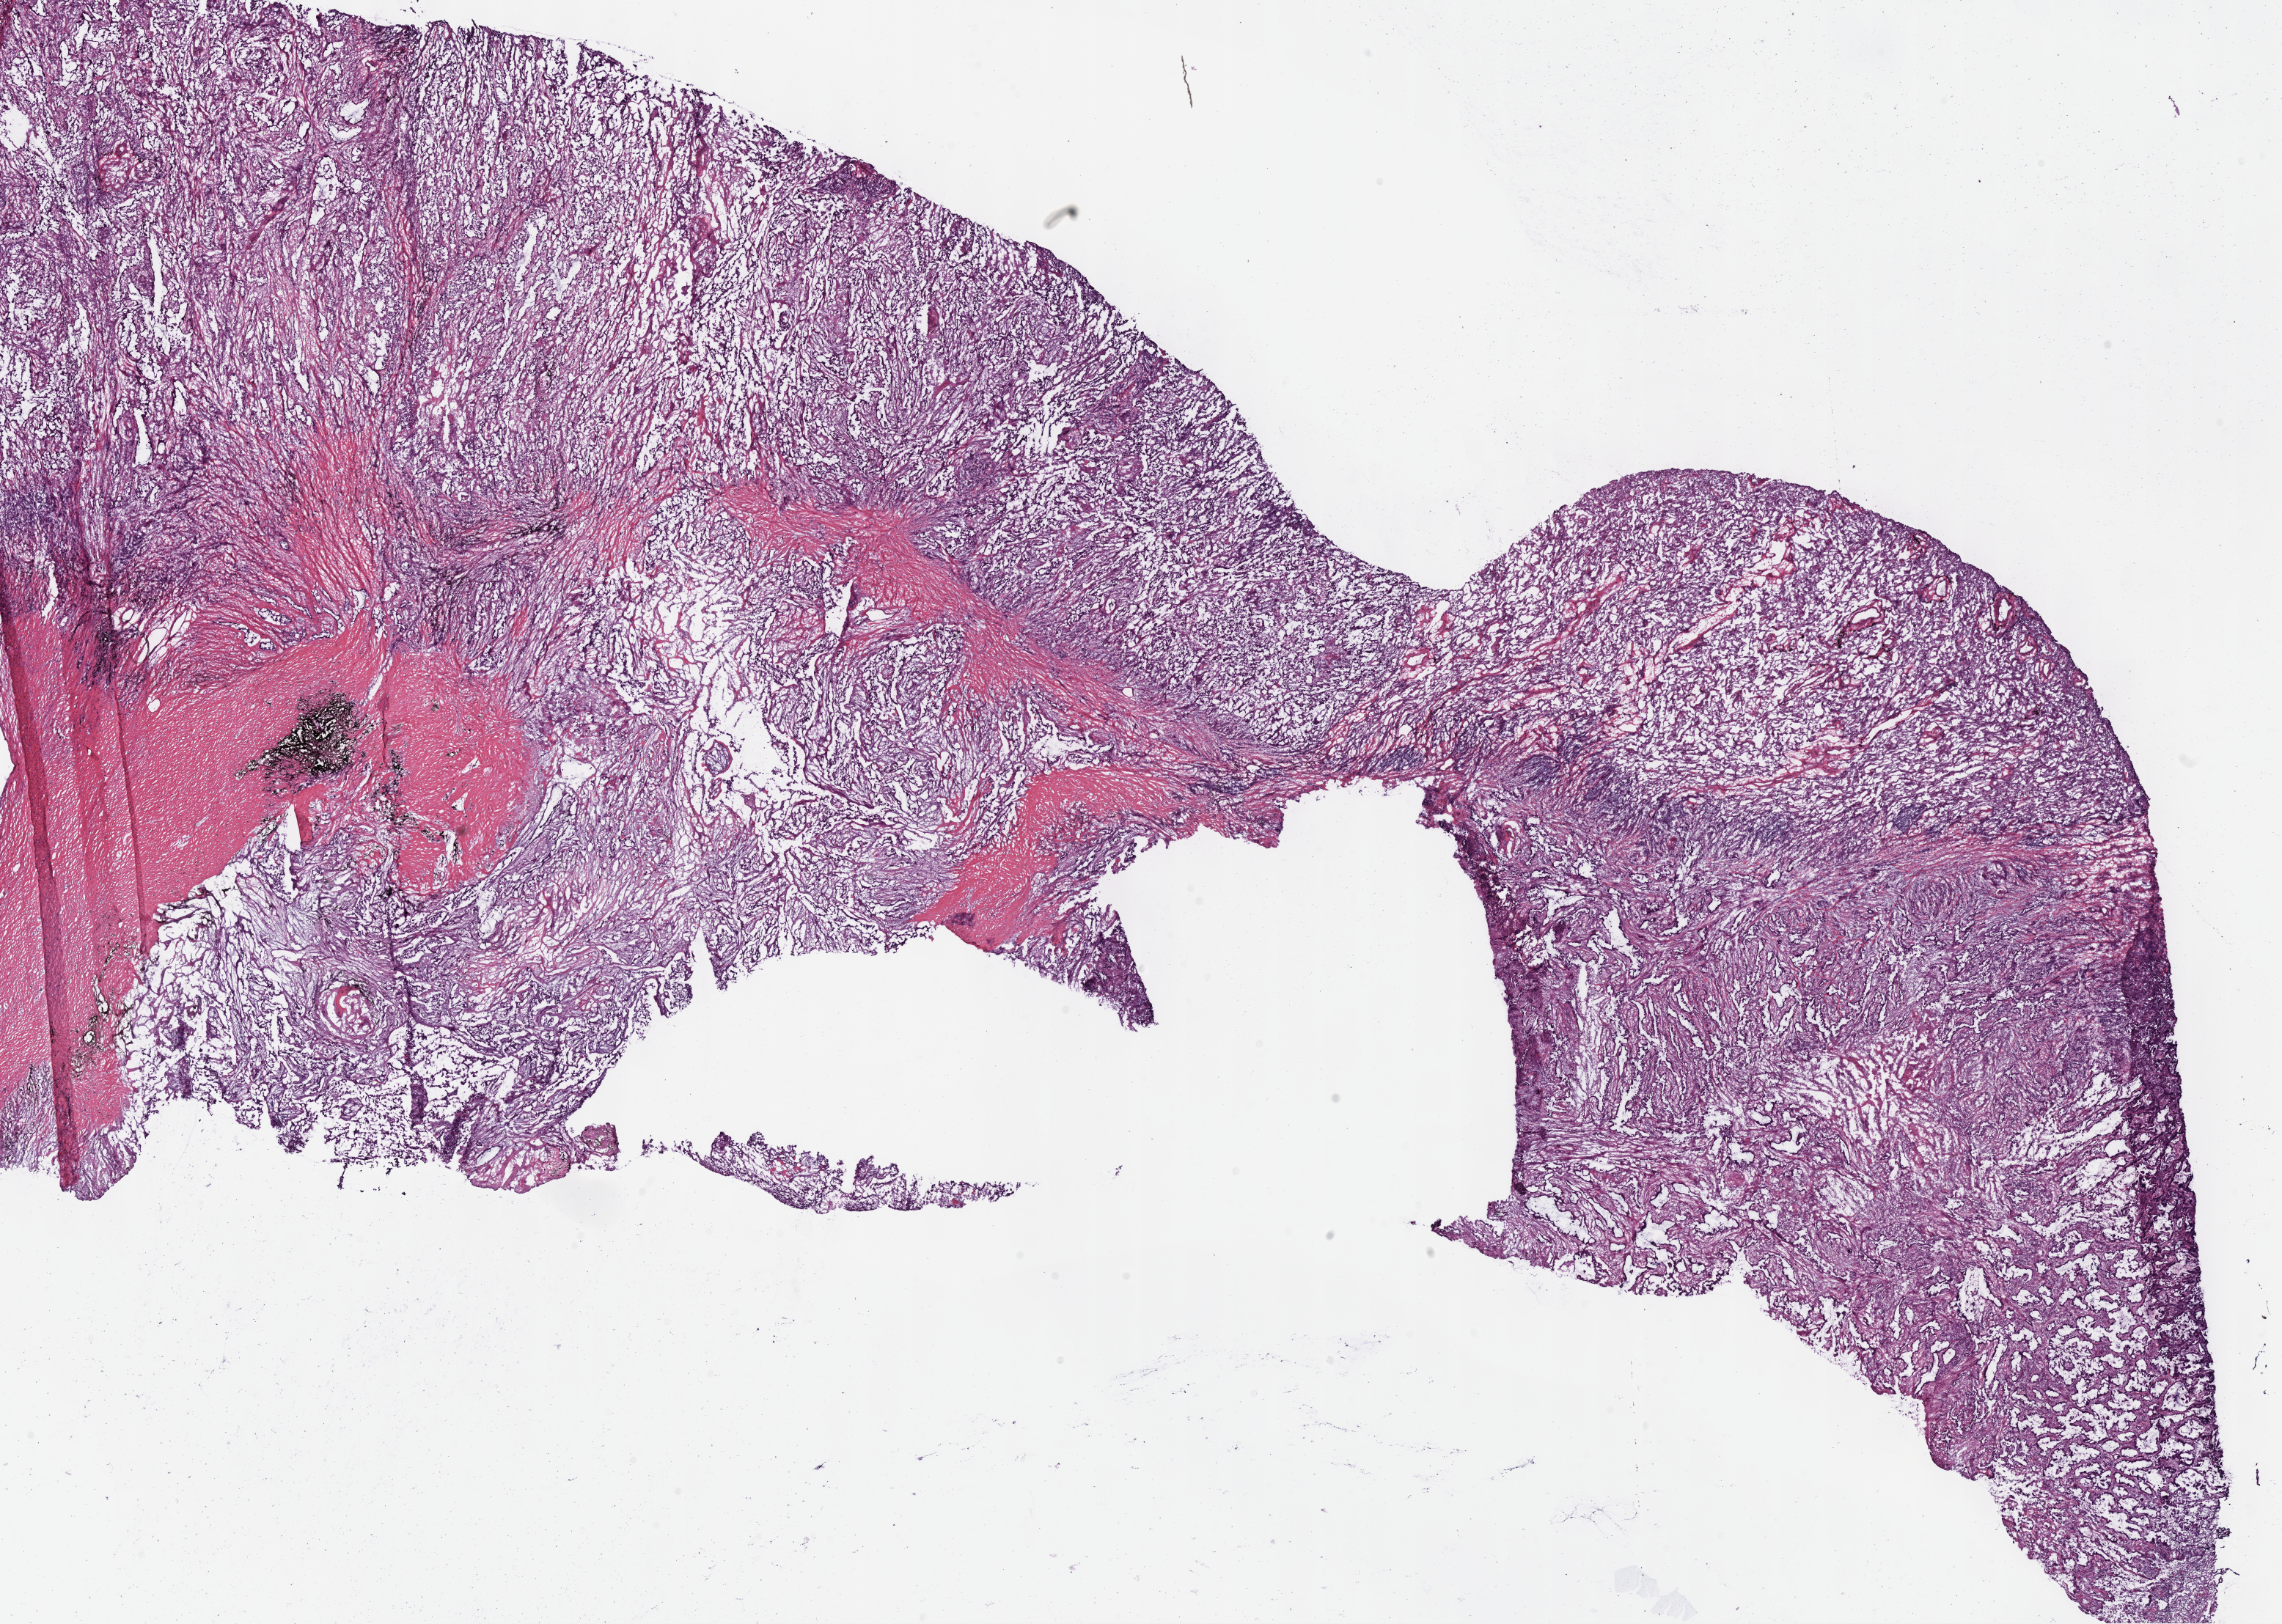
Hematoxylin and eosin (H&E) stained whole-slide image, shown as a low-resolution overview of the whole scanned area (about 24.5 x 17.4 mm, from a 40x scan). Frozen section. Lung, primary tumour sample. Male patient; age at initial diagnosis 79 years. Slide review estimates, as recorded: tumour cells 45%, tumour nuclei 60%, normal cells 7%, stromal cells 45%, necrosis 3%. Infiltration values recorded for this section: lymphocyte infiltration 15%, monocyte infiltration 8%.
- AJCC pathologic stage: IIA (7th edition)
- pathologic diagnosis: Adenocarcinoma, NOS (upper lobe, lung)